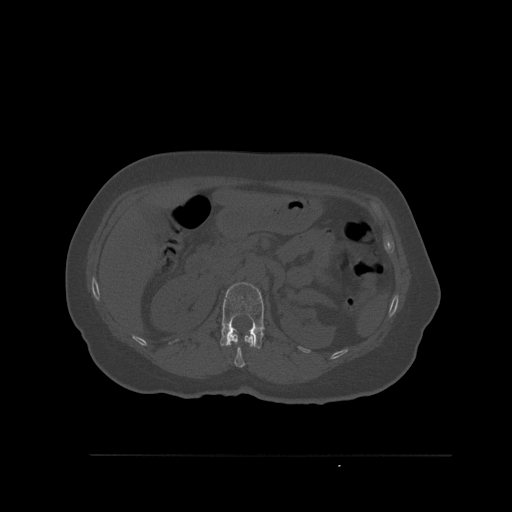
CT including the spine, one axial slice; position 270 of 527 along the scan axis; bone window (W 1800 / L 400 HU); 512 × 512 image matrix, field of view 470 × 470 mm. Female patient, age 73 years. From the clinical record (not read from this slice): primary cancer: breast; vertebrae with lytic lesions (as recorded): L2.
Structures marked on this image (semi-automatically segmented with operator editing):
- L1 vertebra: box from (x=220, y=282) to (x=264, y=349) px
- T12 vertebra: (x=227, y=333)–(x=254, y=368)